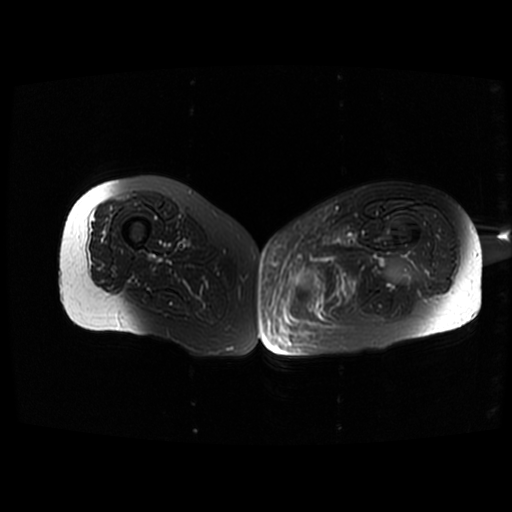
MRI of an extremity soft-tissue mass, one axial slice; position 42 of 42 along the scan axis; T2-weighted fat-saturated; 6 mm slice thickness; 512 × 512 image matrix. Female patient. Case-level facts recorded for this patient, not image findings: histological type: pleomorphic leiomyosarcoma; grade: high; site of the primary tumour: left thigh.
Structures marked on this image (outlined manually by an expert reader):
- gross tumour volume including surrounding oedema: bounding box <293,269,324,292> (left, top, right, bottom; pixels)